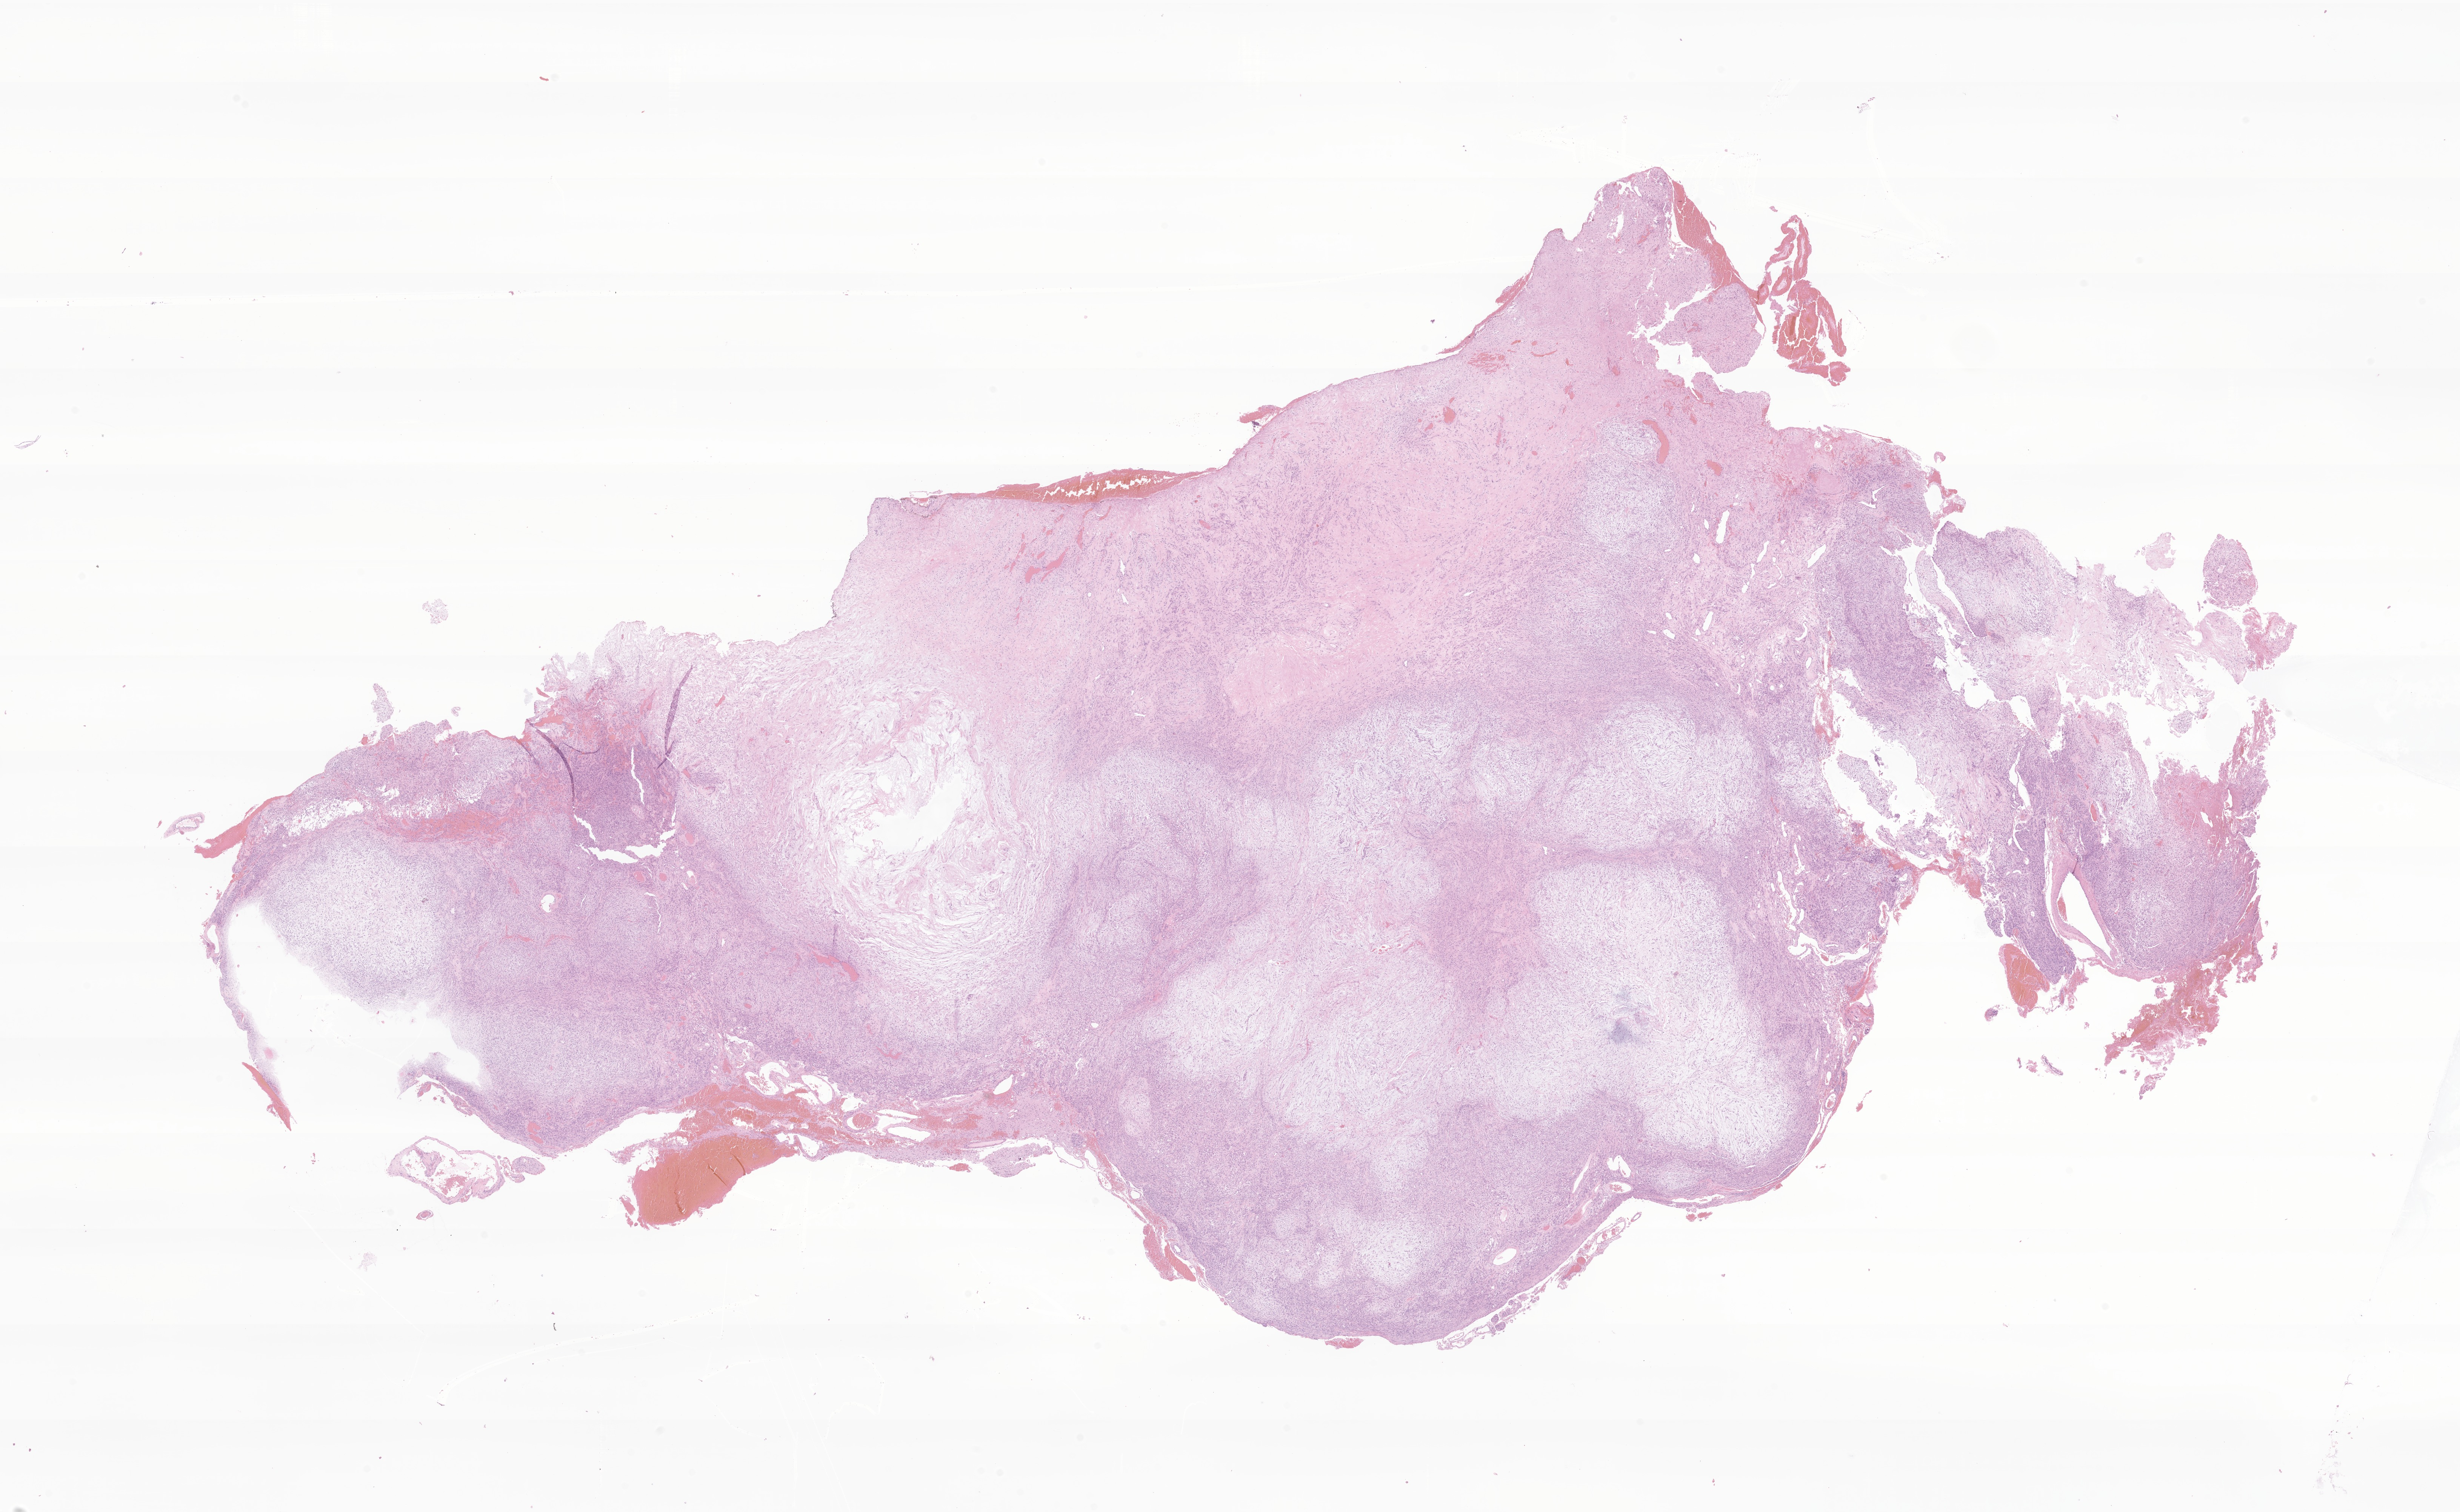
Digitized H&E-stained section of tumor tissue from the brain — shown as a low-resolution overview of the whole scanned area (about 27.5 x 16.9 mm), formalin-fixed, paraffin-embedded (FFPE) tissue. Patient female; age 183 months.
Diagnosis: Meningioma, NOS.